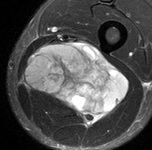
MRI of an extremity soft-tissue mass, one axial slice. Position 45 of 90 along the scan axis. STIR. MR volume resampled by the dataset authors to the PET/CT grid (not the native acquisition matrix). 3.27 mm slice thickness. 152 × 150 image matrix, field of view 148 × 146 mm. Male patient. From the clinical record (not read from this slice): histological type: undifferentiated pleomorphic liposarcoma; grade: high; site of the primary tumour: left thigh.
Outlined on this slice (expert contour drawn on MRI and transferred to this co-registered scan by the dataset authors):
- gross tumour volume including surrounding oedema: bounding box [x1, y1, x2, y2] px = [25, 43, 129, 125]
- gross tumour volume (mass): [25, 43, 129, 125]